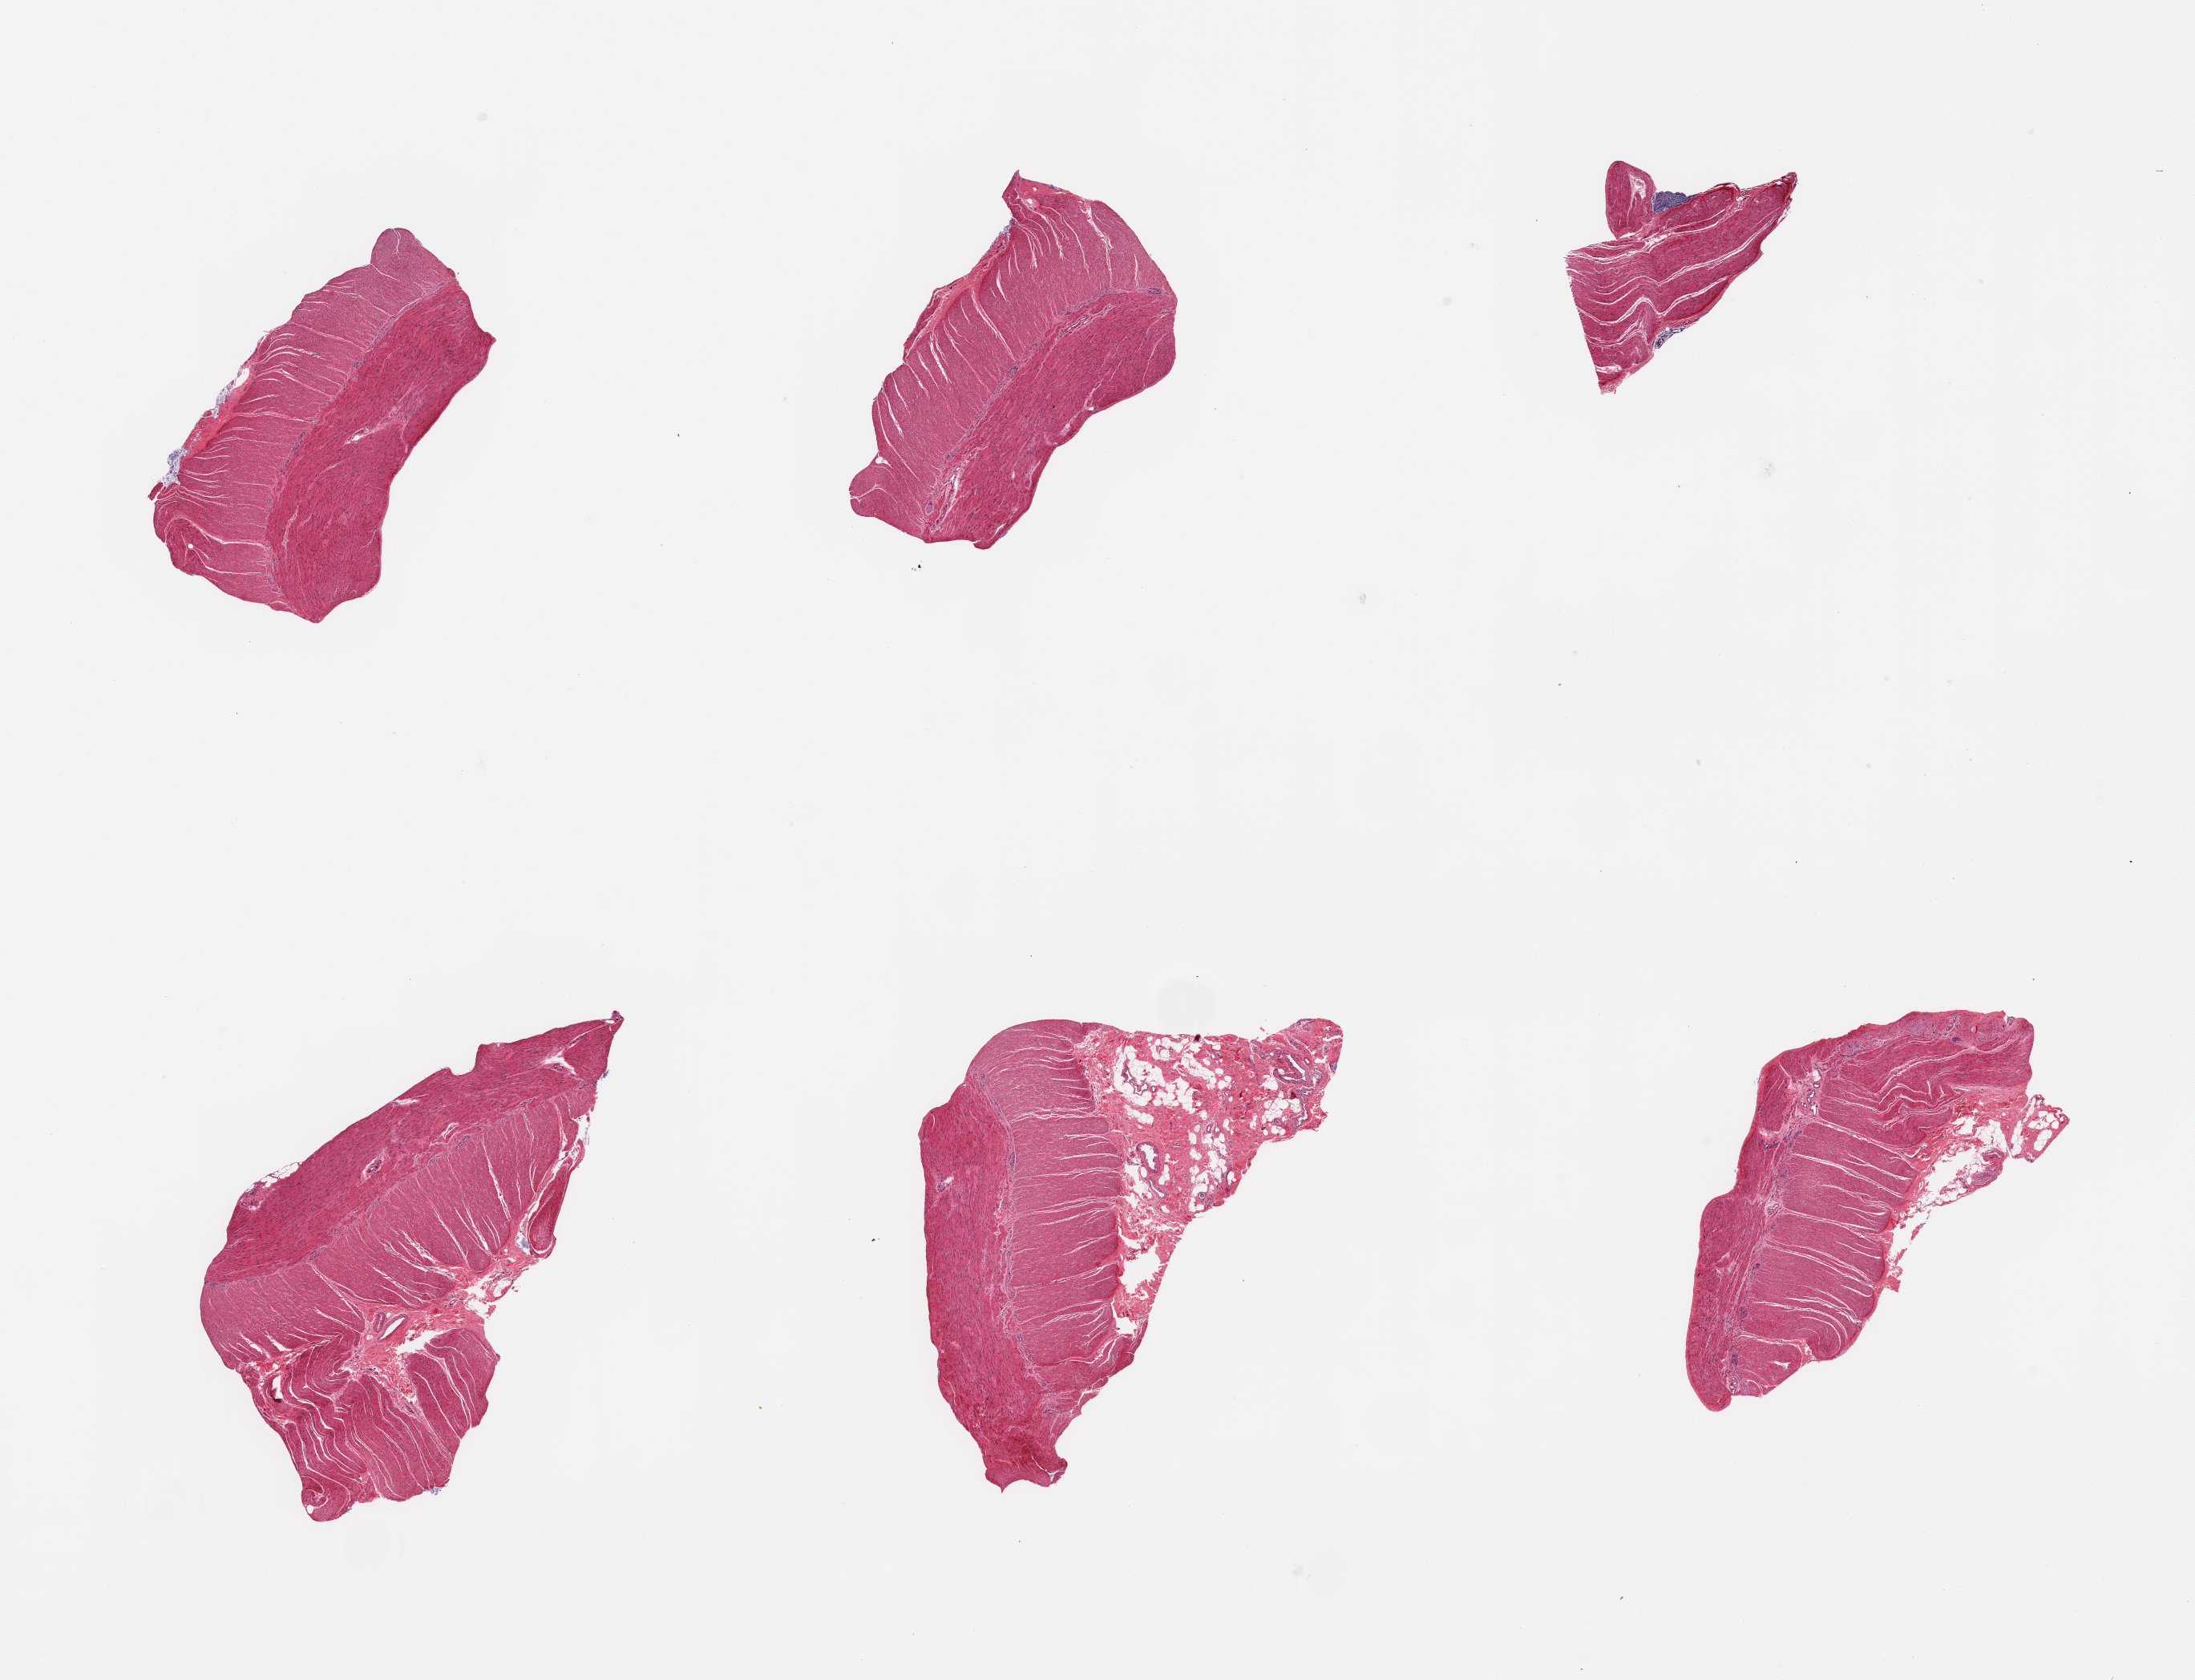
Whole-slide image, hematoxylin and eosin (H&E) stain — whole scanned area (about 21.7 x 16.6 mm, slide scanned at 20x) shown as a low-resolution overview. PAXgene-fixed paraffin-embedded (PFPE) section. Target tissue: sigmoid colon. Tissue donor sample. Male donor.
- pathologist's review note for this sample: 6 pieces; confirmed target muscularis; two pieces with attached serosa